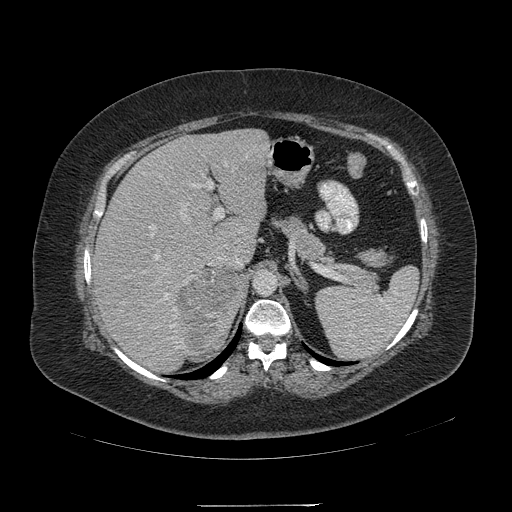
Contrast-enhanced abdominal CT, one axial slice. Intravenous contrast given. Soft-tissue window (W 400 / L 40 HU). 1.25 mm slice thickness. 512 × 512 image matrix, field of view 453 × 453 mm. Patient: female, 55 years. From the clinical record (not read from this slice): diagnosis: adrenocortical carcinoma; tumour side: right adrenal; tumour size at pathology: 11 cm; Ki-67 index: 20 %; stage (as recorded): 2.
Outlined on this slice (semi-automatically segmented with operator editing):
- mass: bounding box [x1, y1, x2, y2] px = [177, 269, 241, 358]